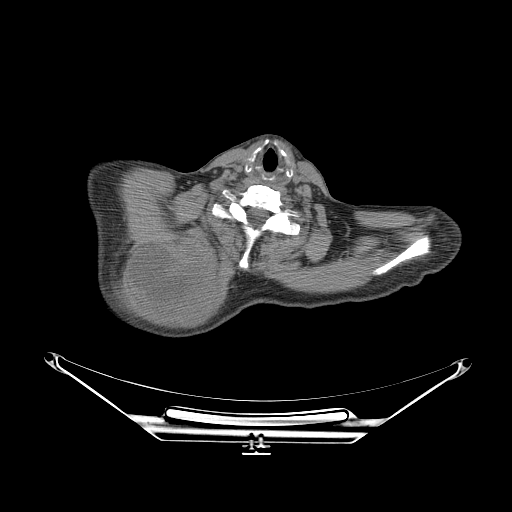
CT of an extremity soft-tissue mass (from a PET/CT study), one axial slice. Position 214 of 267 along the scan axis. 140 kVp. Soft-tissue window (W 400 / L 40 HU). 3.75 mm slice thickness. 512 × 512 image matrix, field of view 500 × 500 mm. Male patient. From the clinical record (not read from this slice): histological type: pleiomorphic spindle cell undifferentiated; grade: high; site of the primary tumour: right parascapusular.
Outlined on this slice (expert contour drawn on MRI and transferred to this co-registered scan by the dataset authors):
- gross tumour volume including surrounding oedema: bounding box (x1, y1, x2, y2) in pixels: (110, 237, 229, 320)
- gross tumour volume (mass): (130, 242, 211, 318)